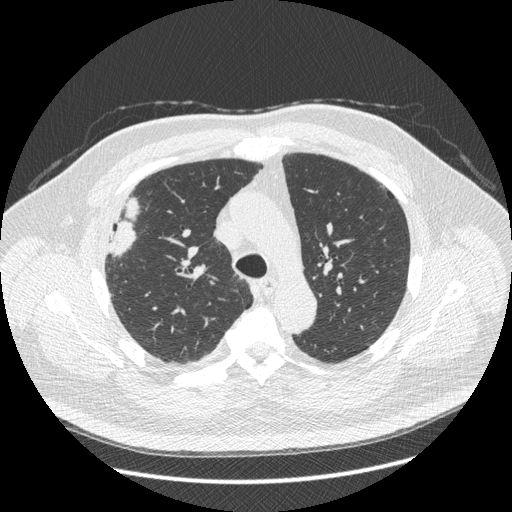
Low-dose screening chest CT, axial slice; third annual screen; lung window (W 1500 / L -600 HU); 1.25 mm slice thickness; standard (soft-tissue) reconstruction kernel (STANDARD); 120 kVp; slice 125 of 426 in the series. Male, age 66 years at enrolment. Current smoker at enrolment.
Expert-annotated lung lesion, bounding box <87,201,147,269> (left, top, right, bottom; pixels). Reader record for this screening exam (exam-level; its link to the box is not recorded): non-calcified nodule or mass ≥4 mm, right upper lobe, 48 × 25 mm, spiculated (stellate) margins, soft tissue attenuation, pre-existing on the prior screen: no. Official screen result: positive, other. Later outcome: lung cancer diagnosed 35 days after this screen — non-small cell carcinoma, right upper lobe, stage IV (AJCC 6th edition), 50 mm at pathology.